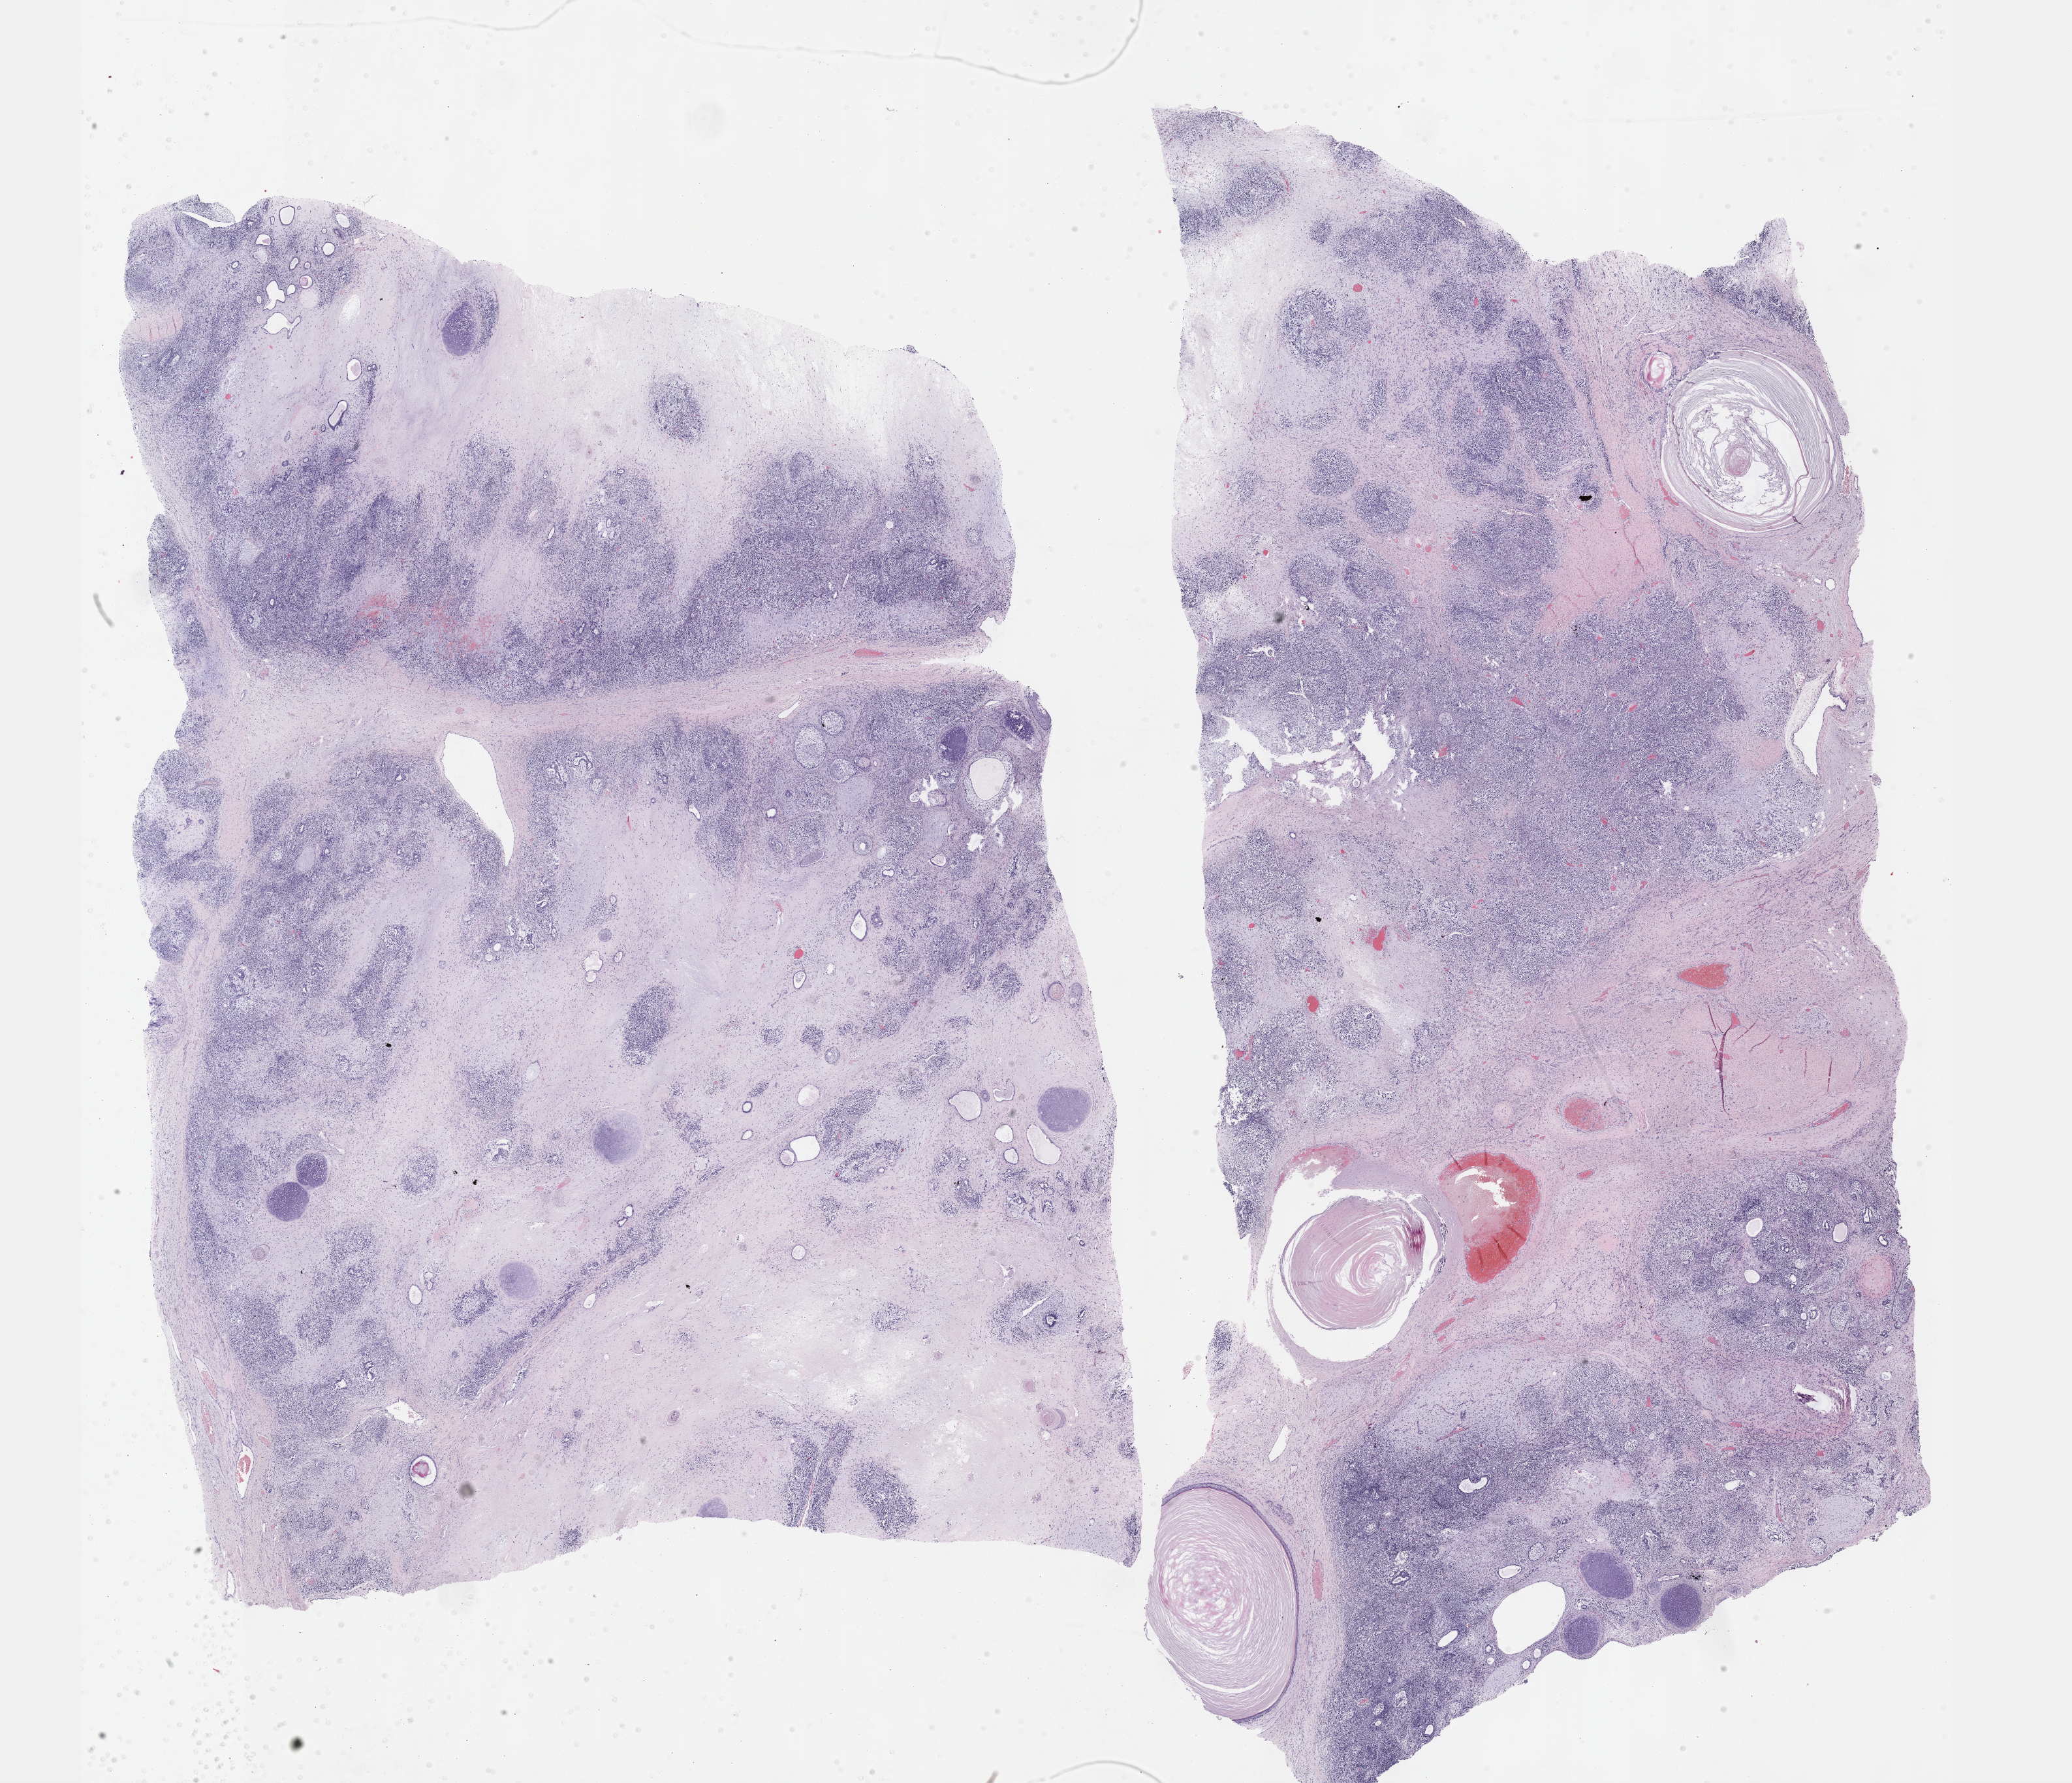
Whole-slide histology image, H&E — low-resolution overview of the scanned area, about 25.7 x 22.1 mm, FFPE section, testis, primary tumour sample. Patient: male, age at initial diagnosis 21 years.
- AJCC pathologic stage: IS
- diagnosis: Mixed germ cell tumor